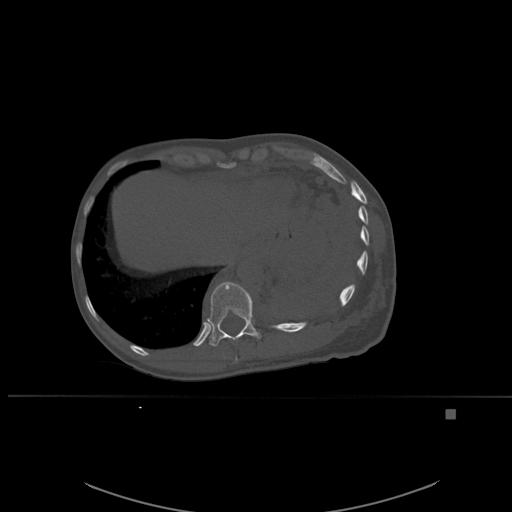
CT including the spine, one axial slice; position 302 of 537 along the scan axis; bone window (W 1800 / L 400 HU); 1.5 mm slice thickness; 512 × 512 image matrix, field of view 440 × 440 mm. Female patient, age 45 years. From the clinical record (not read from this slice): primary cancer: lung.
Structures marked on this image (semi-automatically segmented with operator editing):
- T10 vertebra: bounding box <235,357,237,362> (left, top, right, bottom; pixels)
- T11 vertebra: <207,281,261,346>